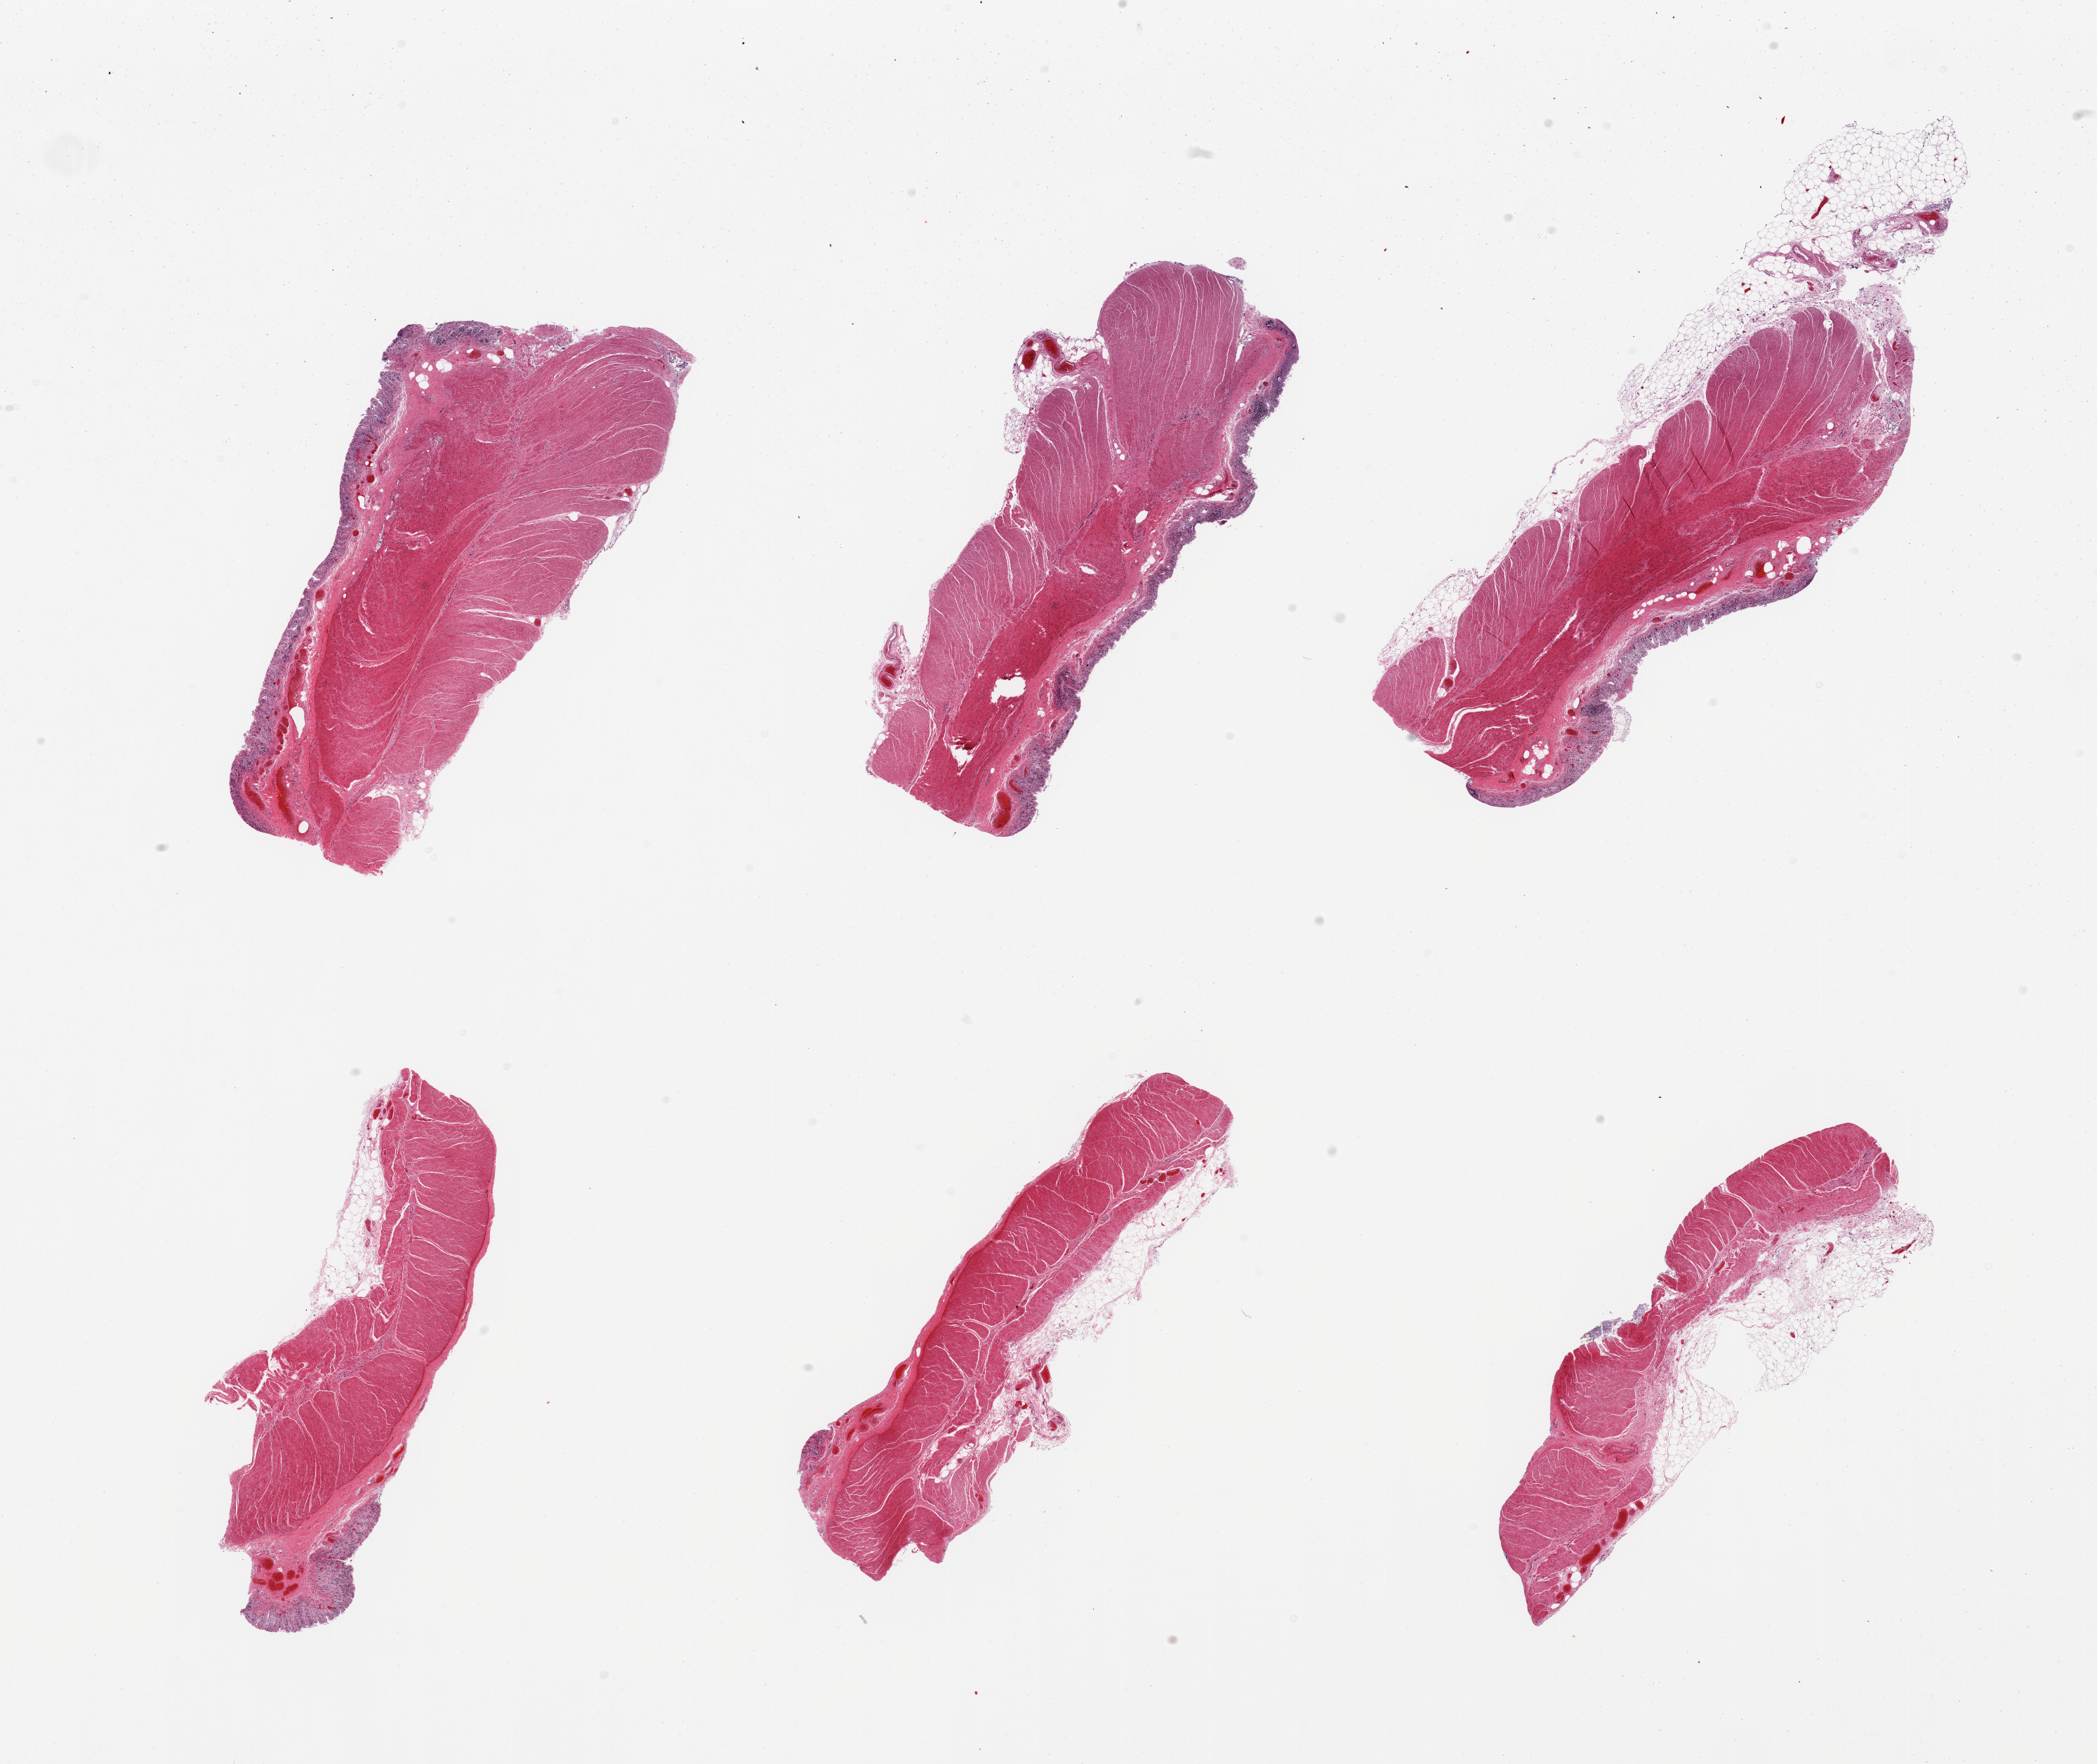
Whole-slide image, H&E stain, brightfield — low-resolution overview of the scanned area, about 23.6 x 19.9 mm, PAXgene-fixed, paraffin-embedded tissue, sampled site (target tissue): transverse colon, tissue donor sample. Female donor.
Review note (as recorded): 6 piece, glandular mucosa completely autolyzed; lamina prpria remnants are ~0.25mm.